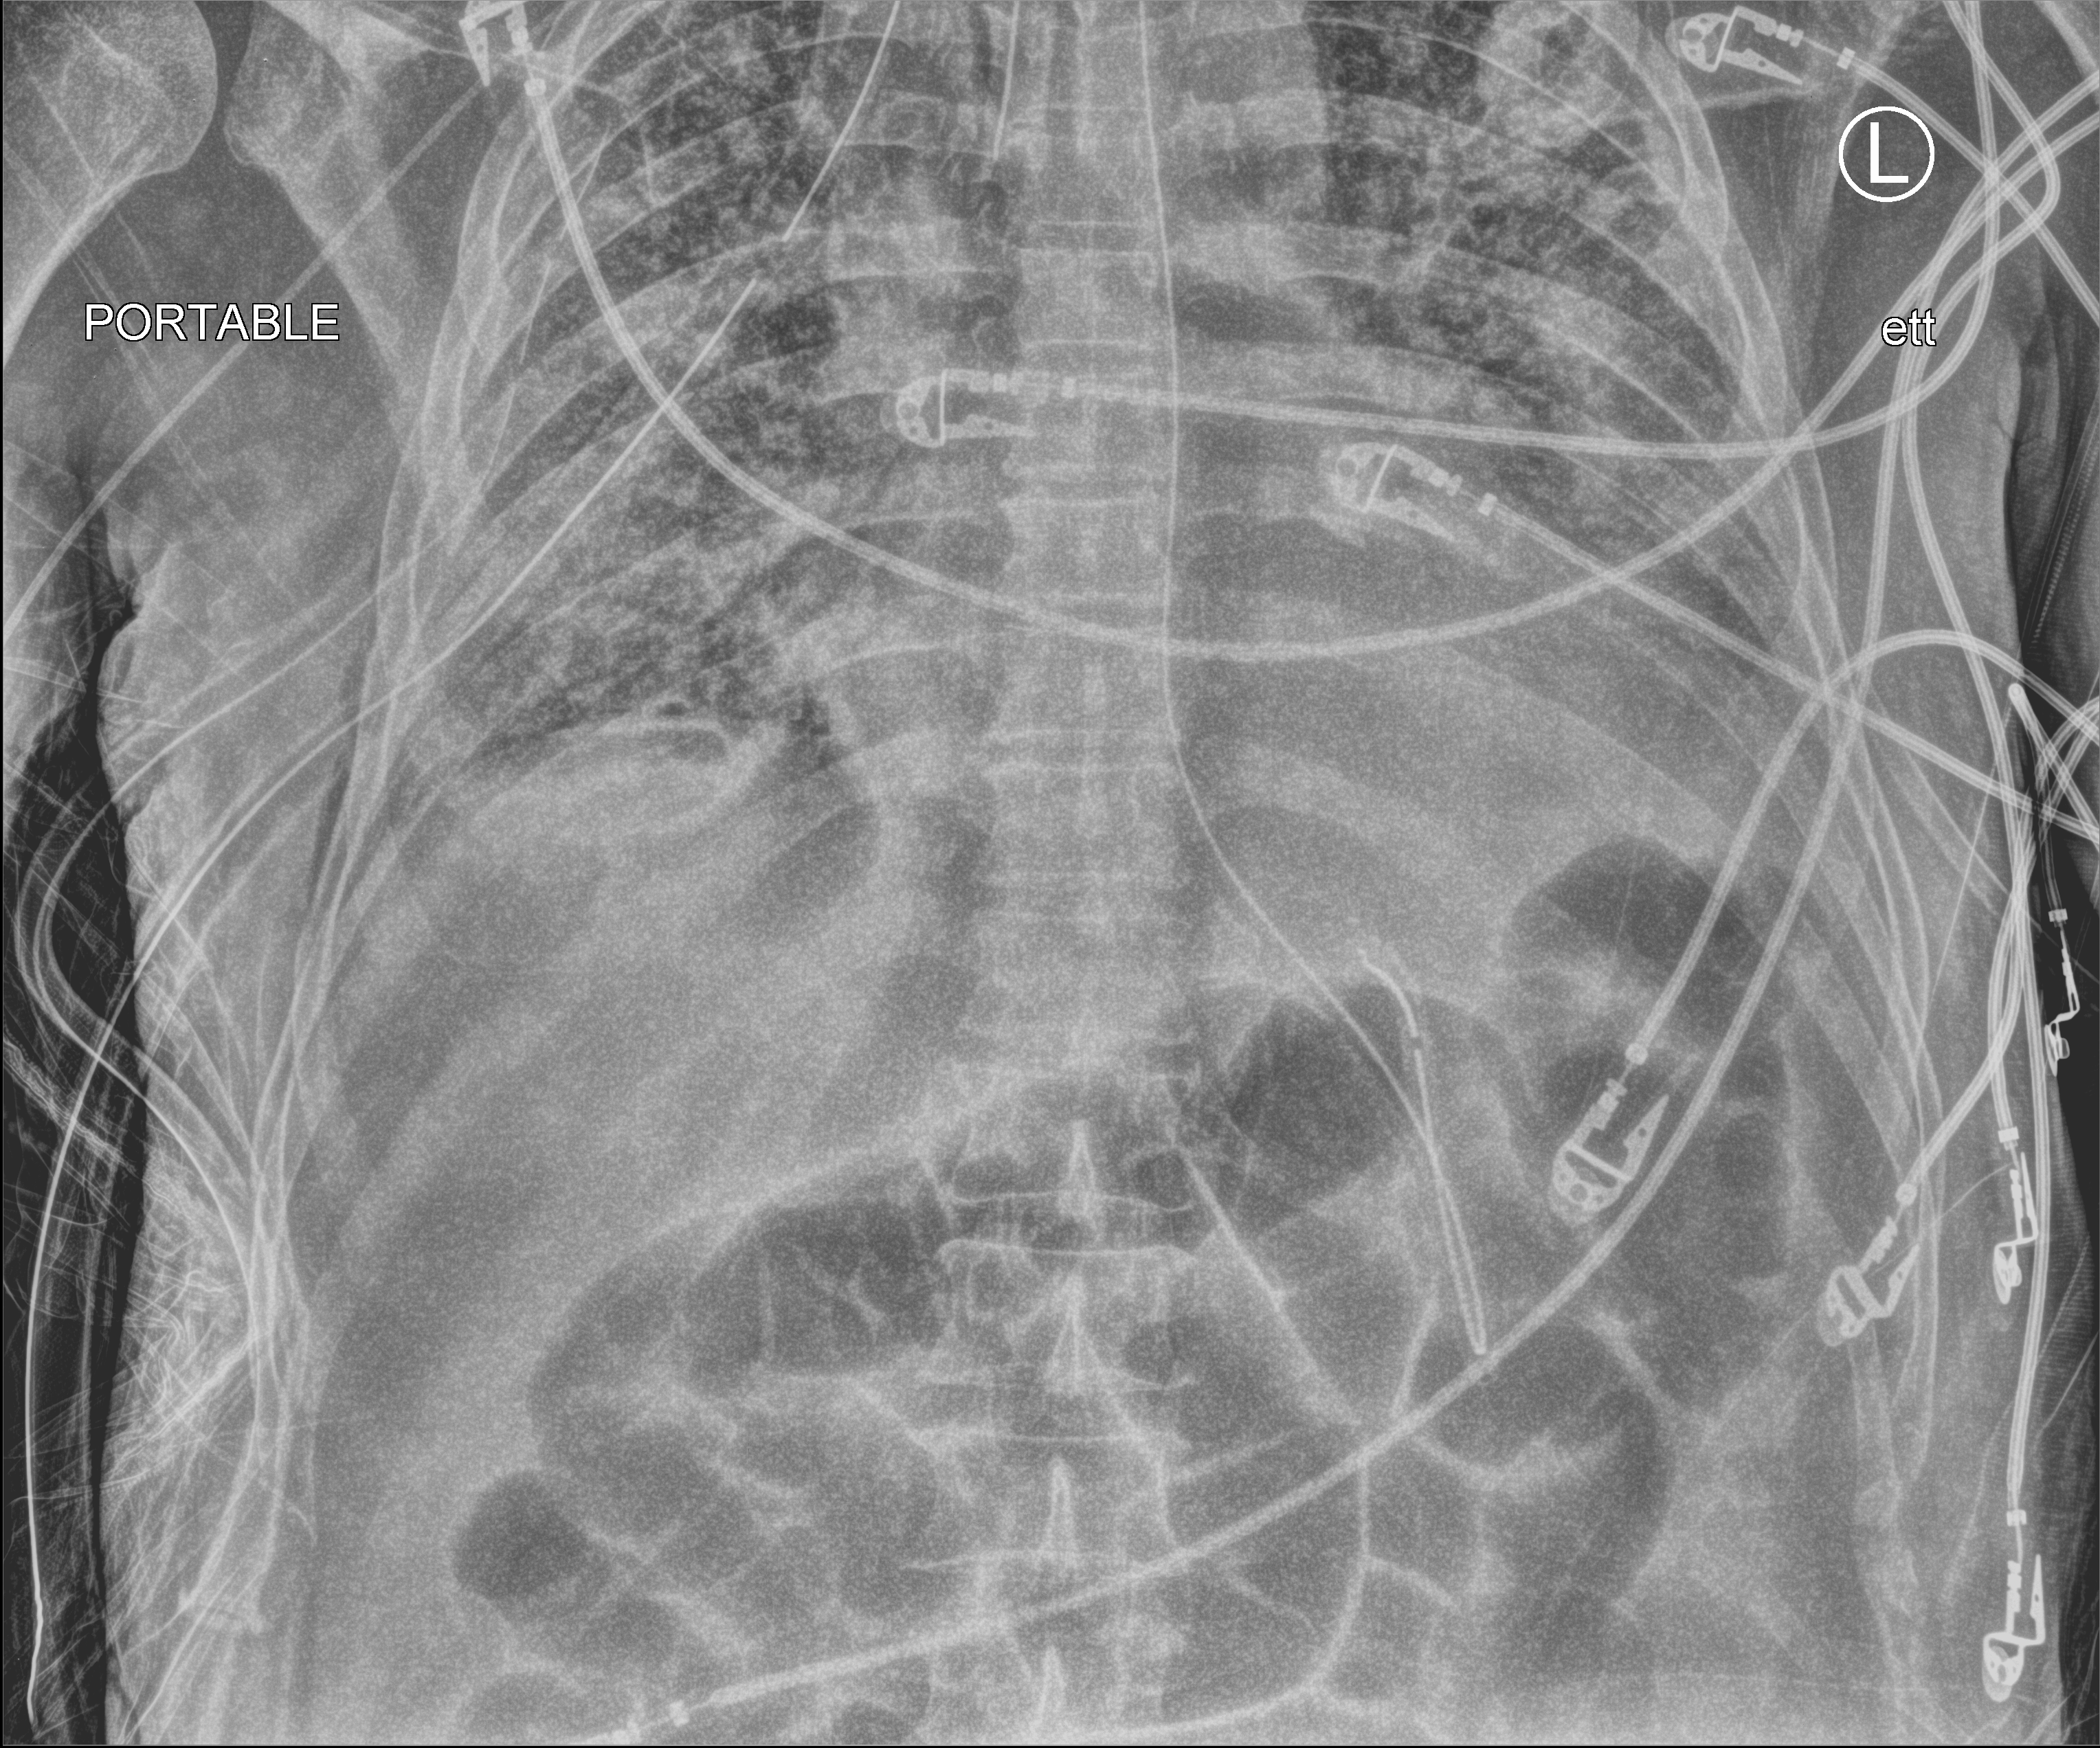
Bedside chest radiograph (computed radiography). Patient hospitalised with COVID-19; male, aged 60–74 years.
From the hospital-stay record, not from the radiograph (when in the stay this image was taken is not recorded): COPD (admission record): no; admitted to intensive care during this hospital stay: yes; mechanically ventilated during this hospital stay: yes.